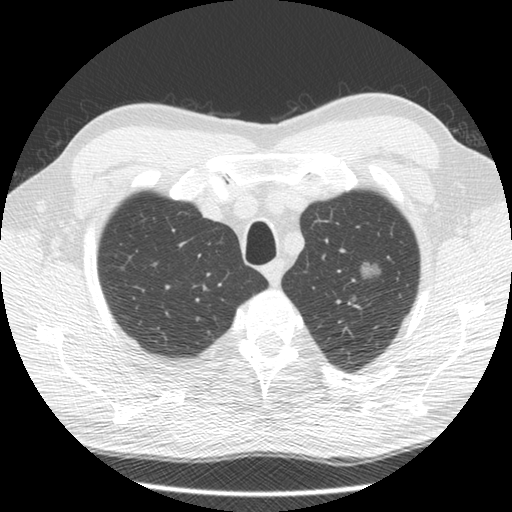
Low-dose screening chest CT, one axial slice. Slice 114 of 132 in the series (ordered by position). Reconstruction kernel STANDARD. 120 kVp. Lung window (W 1500 / L -600 HU). 512 × 512 image matrix.
Outlined on this slice (expert manual segmentation):
- lesion 1 (tumor, upper lobe of left lung): box from (x=354, y=262) to (x=380, y=282) px